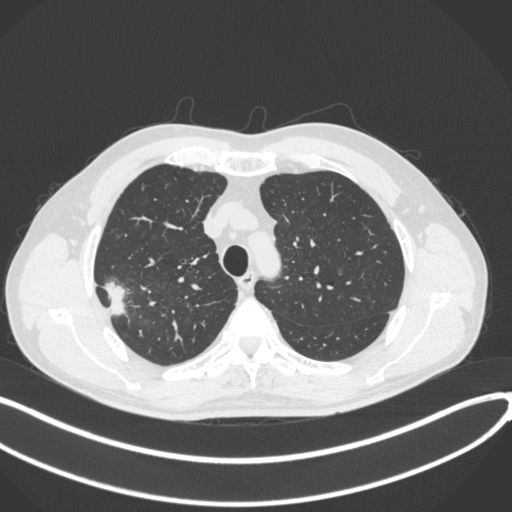
Chest CT, one axial slice; position 325 of 381 along the scan axis; reconstruction kernel B31f; 120 kVp; lung window (W 1500 / L -600 HU); 1 mm slice thickness; 512 × 512 image matrix, field of view 400 × 400 mm. Patient: male, 62 years. Case-level facts recorded for this patient, not image findings: clinical TNM (as recorded): T1c N0 M0.
Structures marked on this image (bounding box drawn by a radiologist):
- lung tumour (recorded histology: adenocarcinoma): bounding box [x1, y1, x2, y2] px = [102, 280, 128, 316]